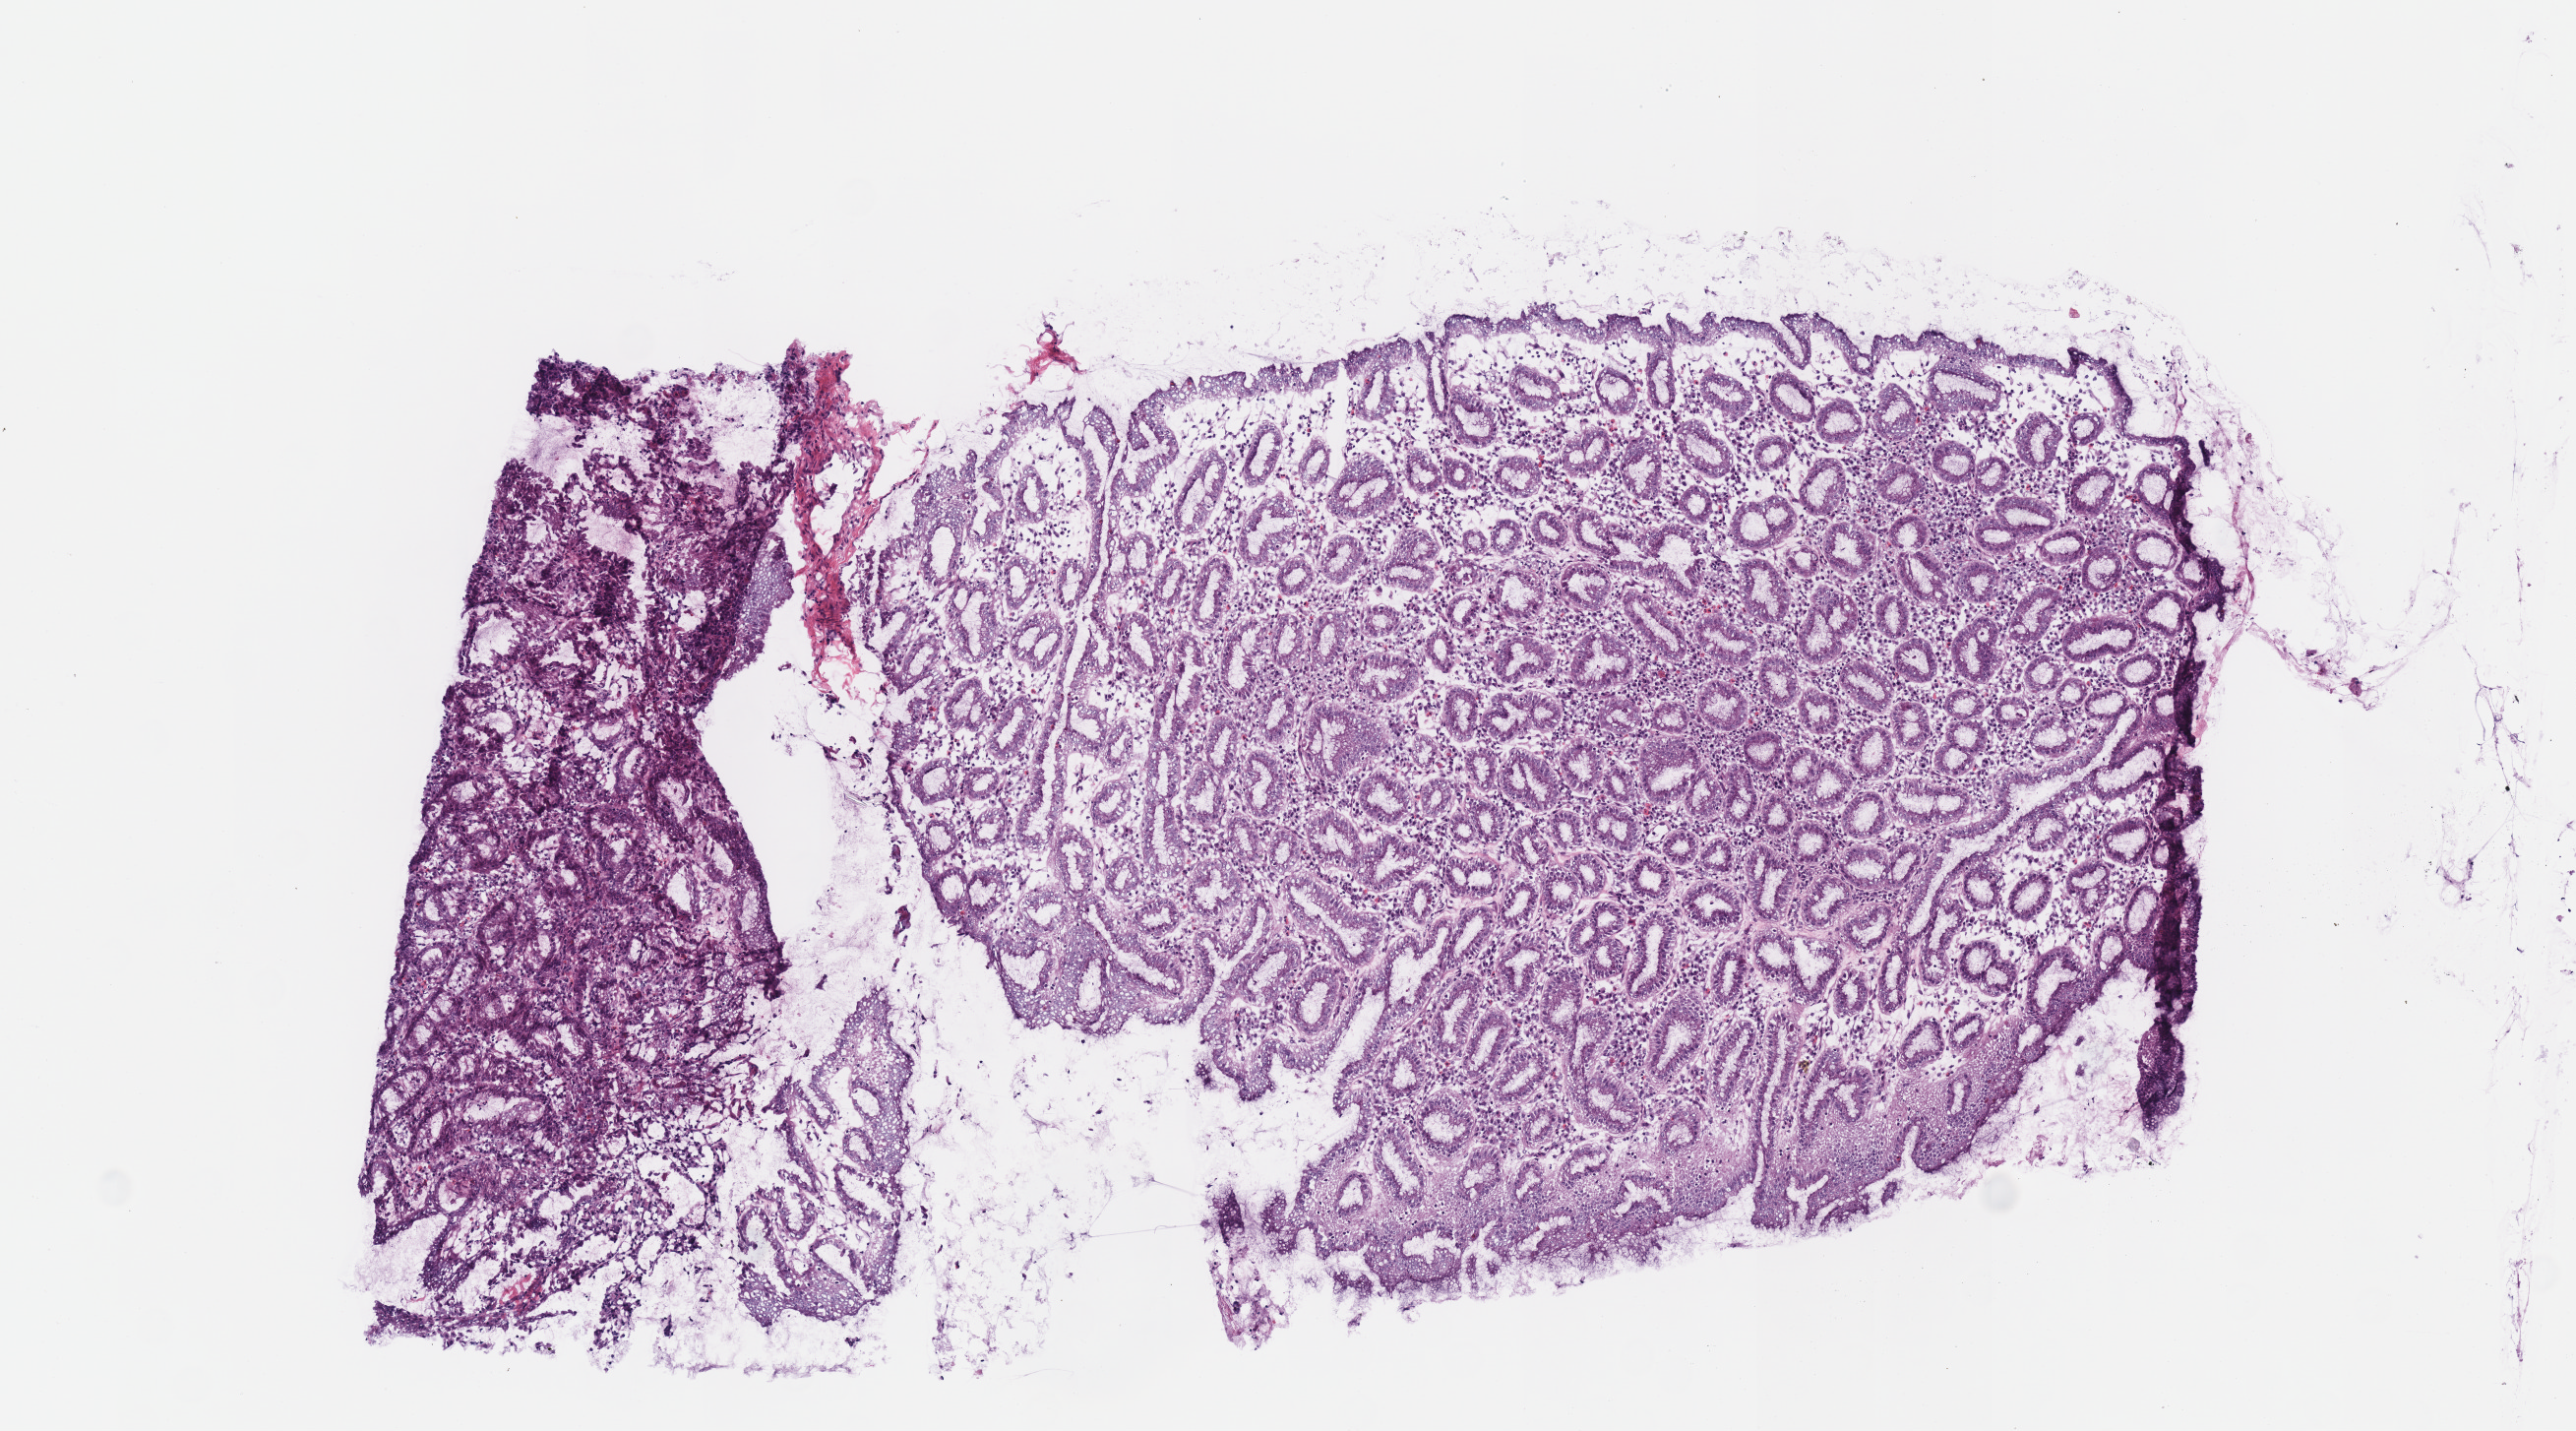
H&E-stained whole-slide image, shown as a low-resolution overview of the whole scanned area (about 5.2 x 2.9 mm, acquisition: 40x scan). Frozen section from the top of the tissue portion. Stomach, solid tissue normal (non-tumour tissue) sample. Male, age 66 years at initial diagnosis.
This section: solid tissue normal sample (biorepository sample class). Patient diagnosis: Tubular adenocarcinoma.